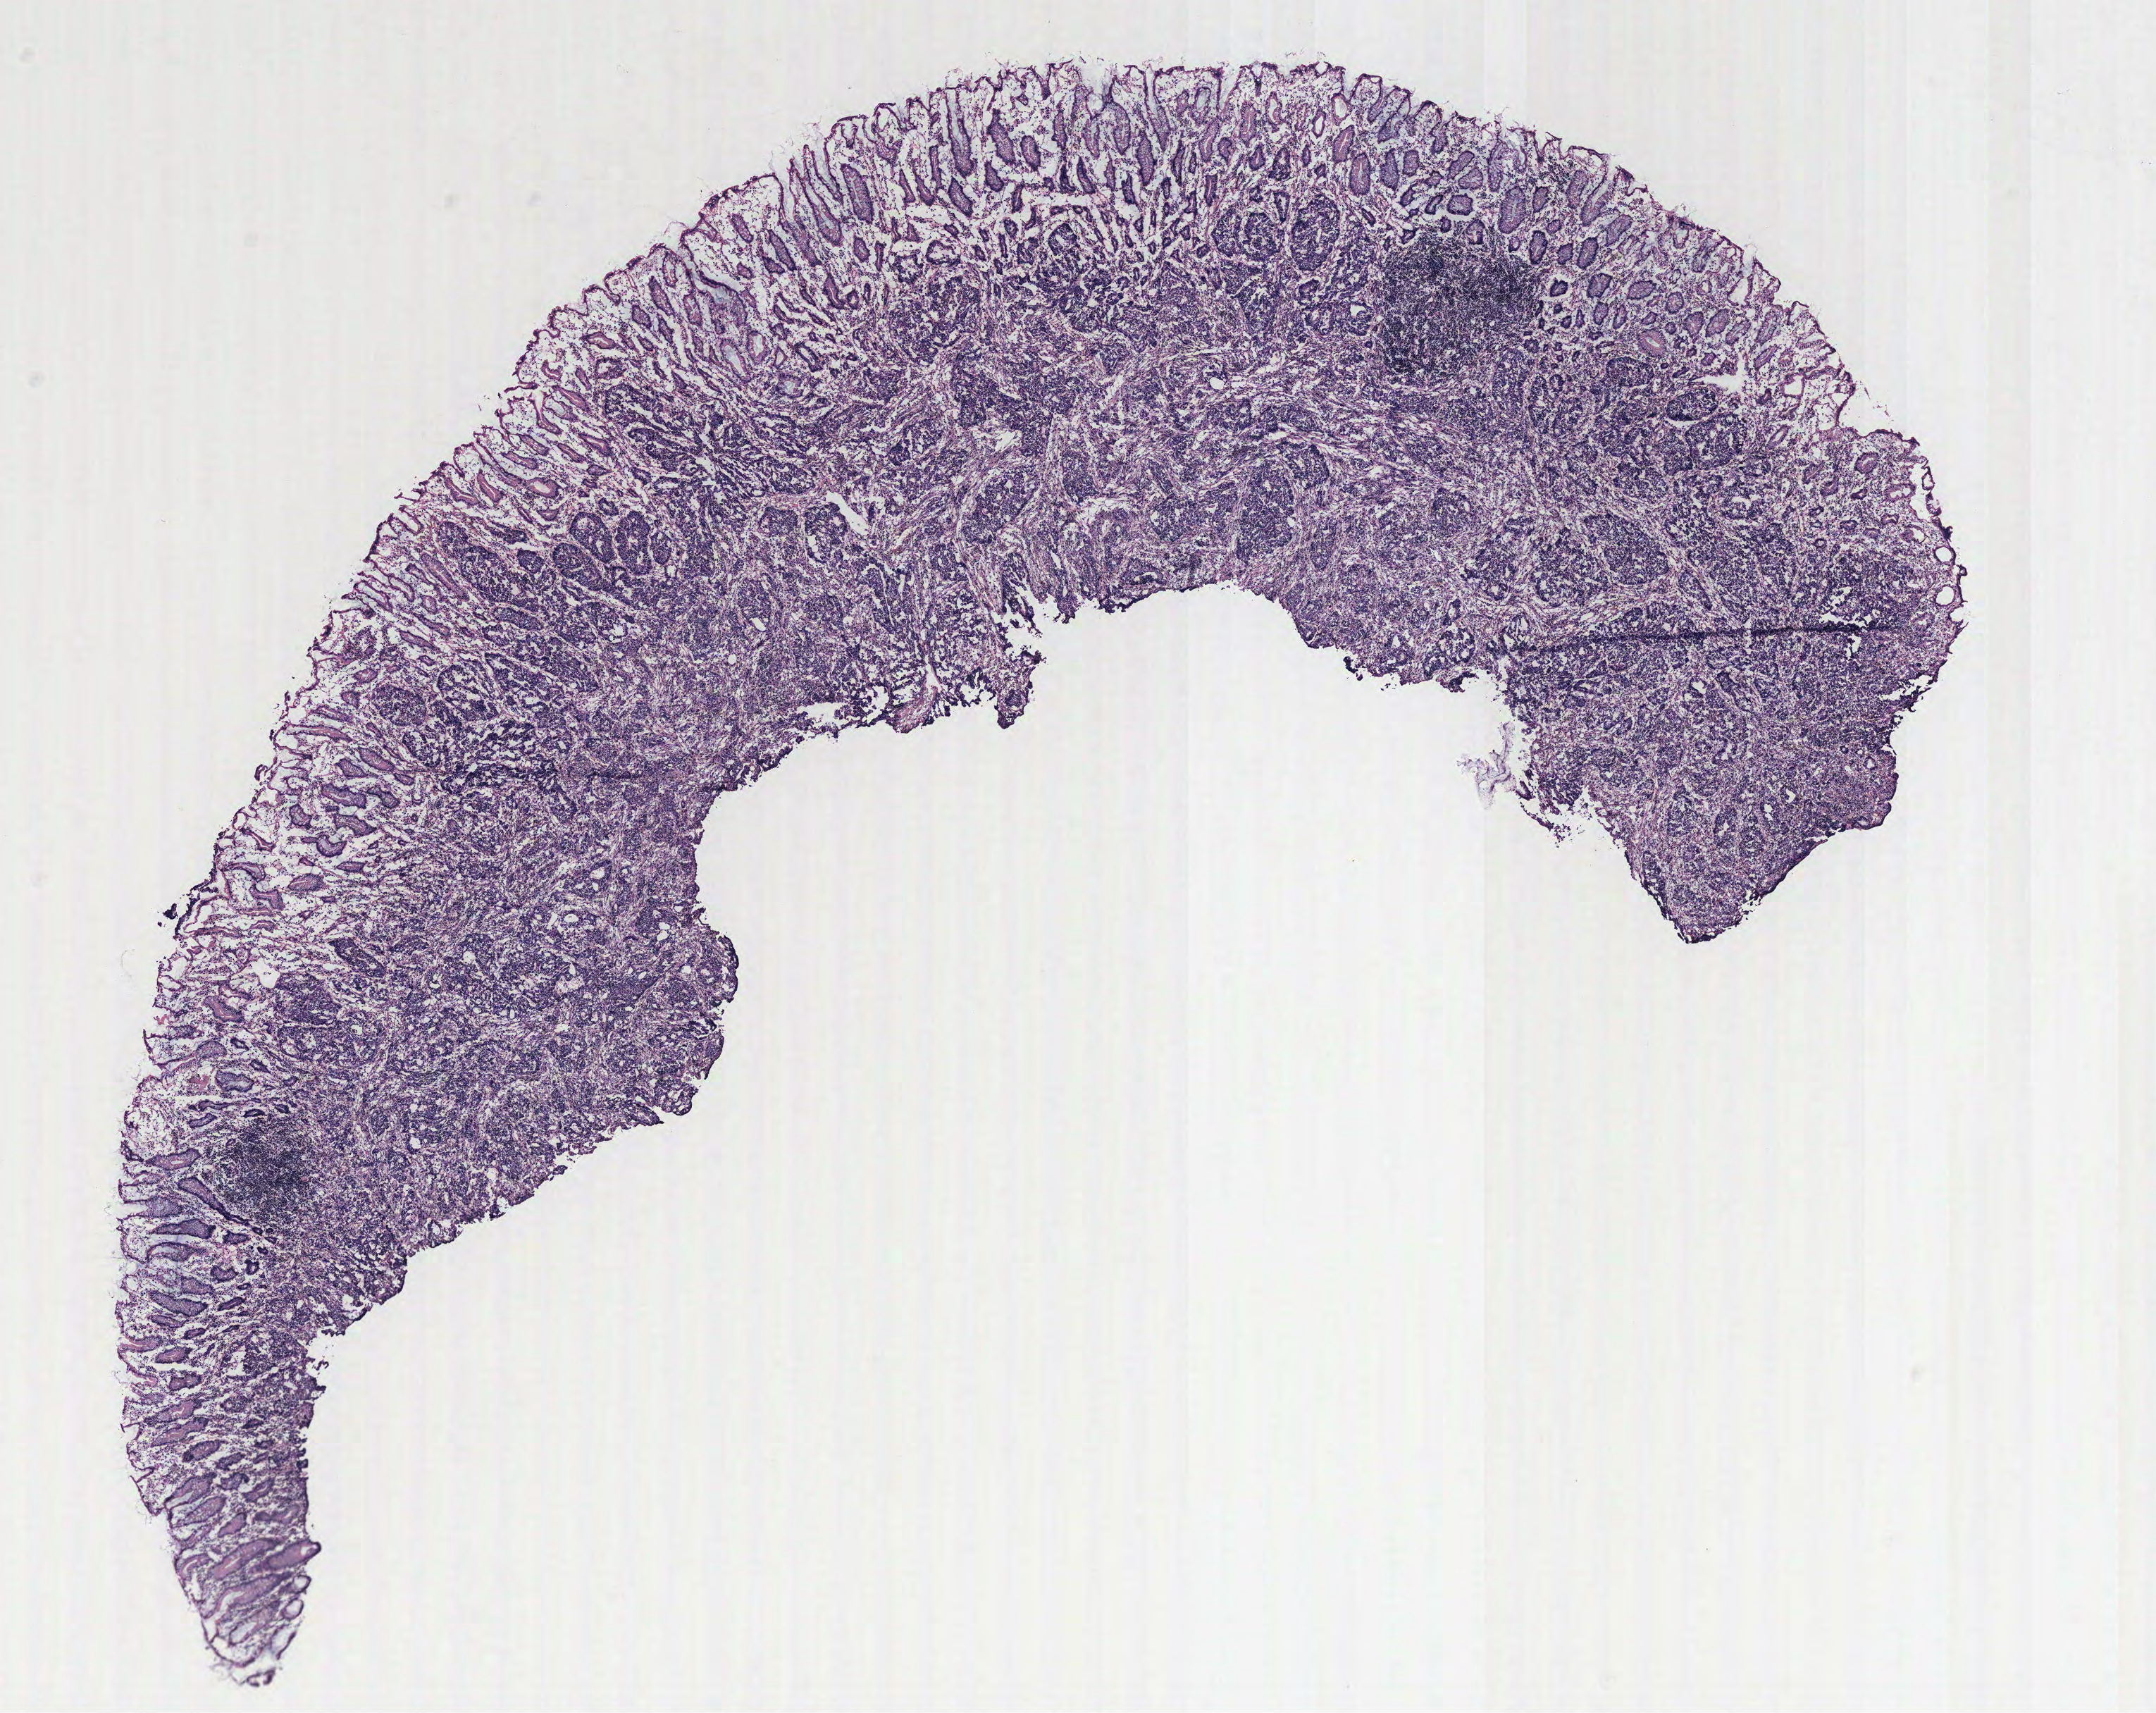
Whole-slide histology image, Hematoxylin and eosin (H&E) stained — shown as a low-resolution overview of the whole scanned area (about 12.2 x 9.7 mm), normal (non-tumour) tissue sample, colon. Male, 87 y/o.
This section: normal (non-tumour) tissue from the same patient. Patient diagnosis: Adenocarcinoma, NOS.